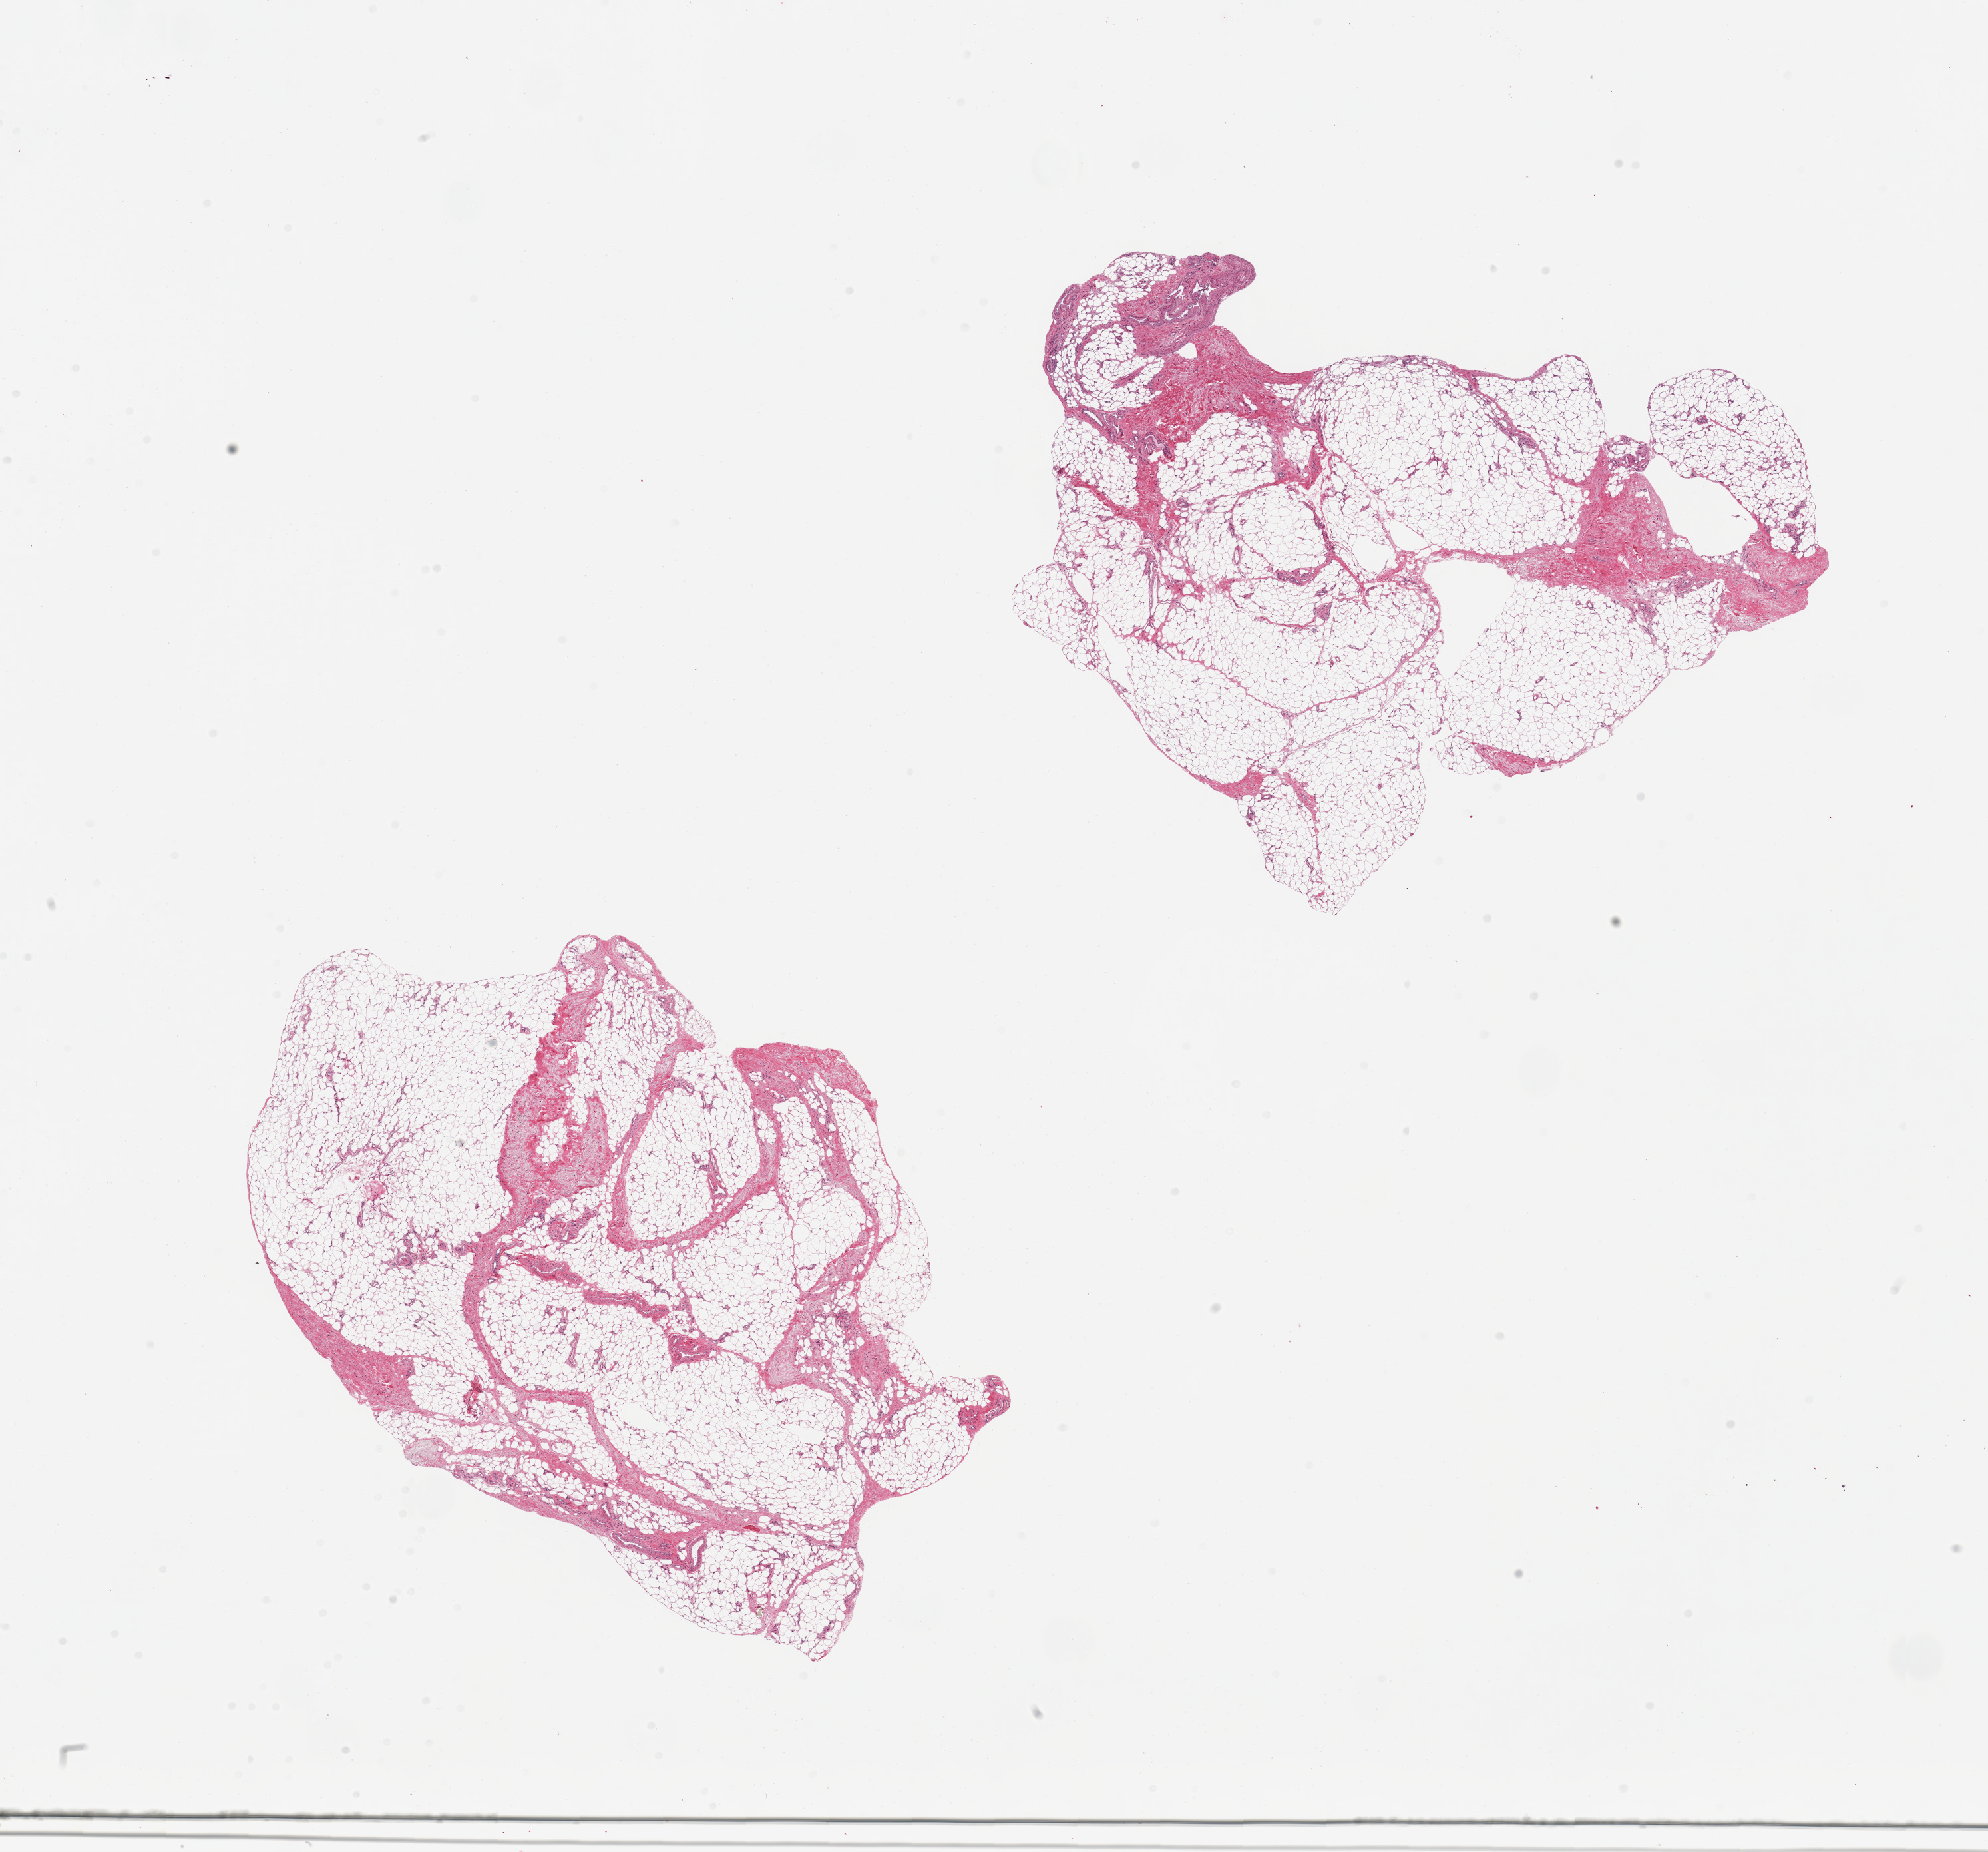
Digitized haematoxylin and eosin-stained section — shown as a low-resolution overview of the whole scanned area (about 23.6 x 22.0 mm). PAXgene-fixed, paraffin-embedded tissue. Target tissue: adipose tissue. Tissue donor sample. Donor: female.
• review note (as recorded): 2 pieces, ~20% fascia/vascular tissue